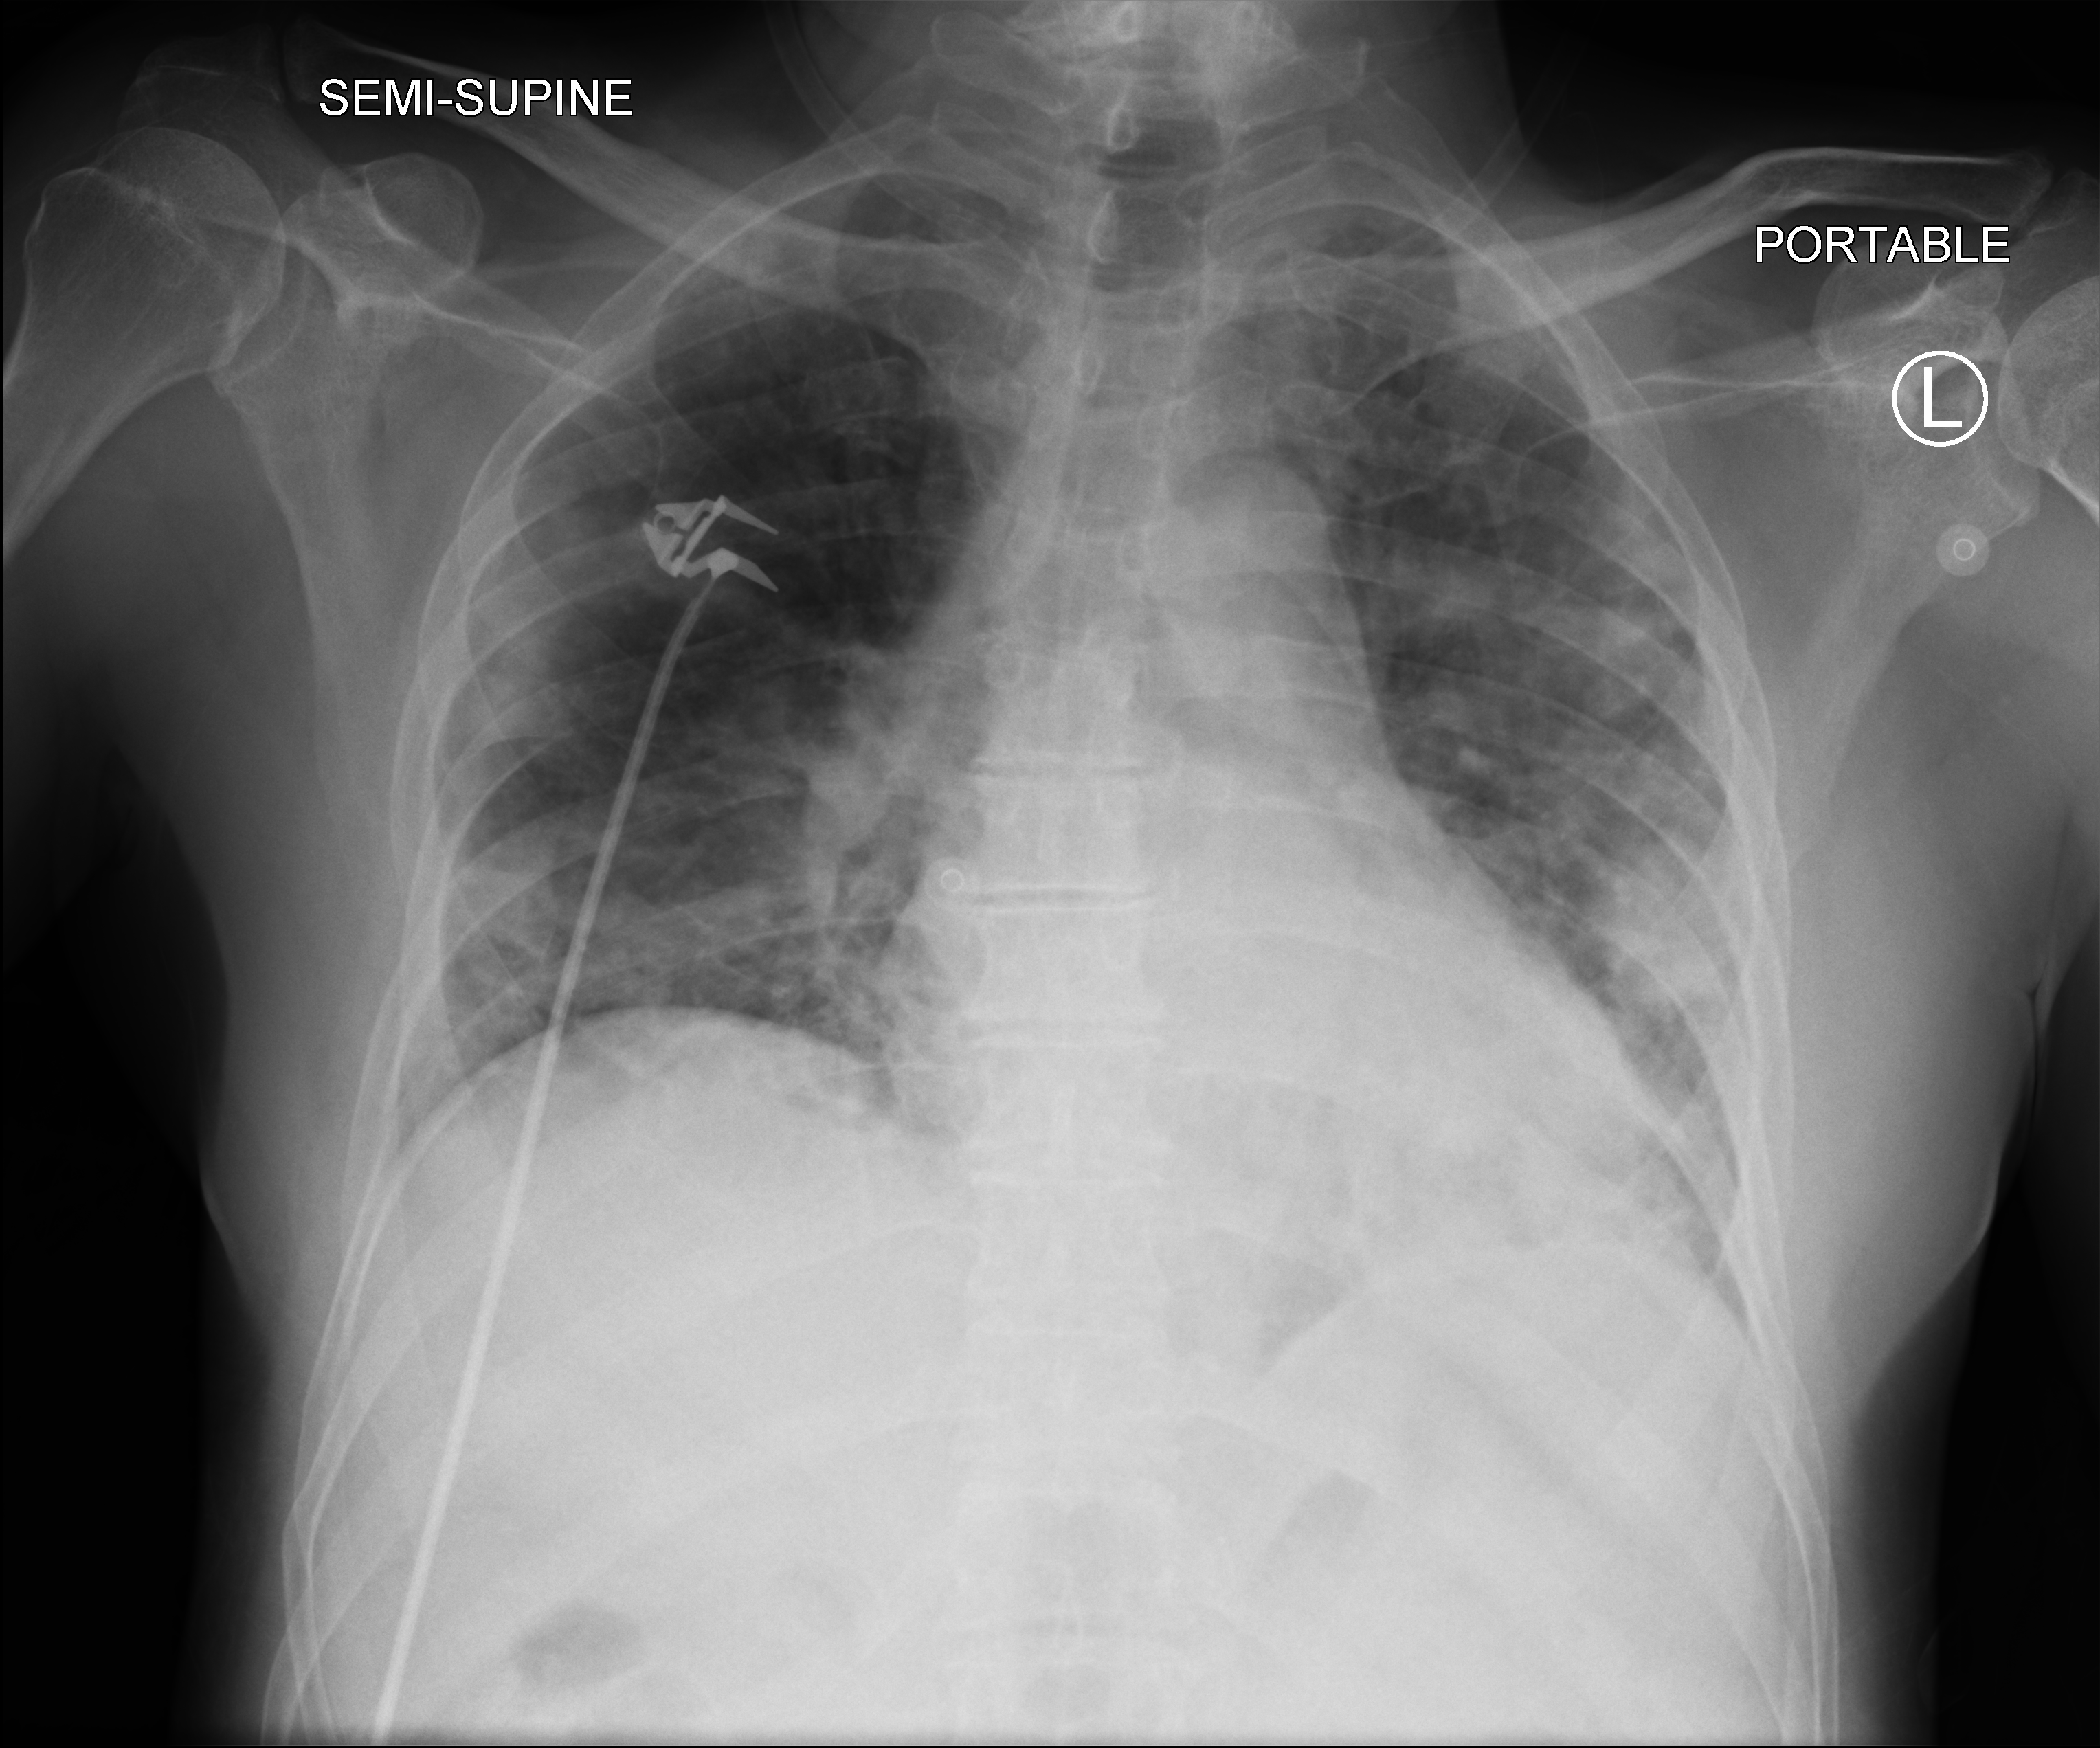
Portable chest radiograph; anteroposterior (AP) projection. Male patient hospitalised with COVID-19, age 60–74 years.
Admission-level facts for this patient (not findings on this image; timing relative to this image not recorded):
- admitted to intensive care during this hospital stay: no